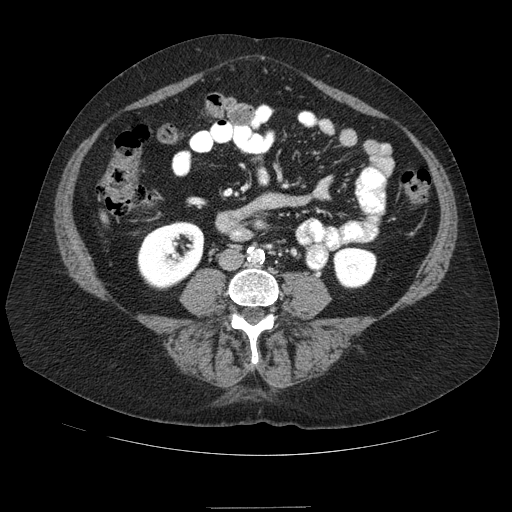
Contrast-enhanced abdominal CT (liver protocol), one axial slice; position 8 of 89 along the scan axis; reconstruction kernel STANDARD; 120 kVp; soft-tissue window (W 400 / L 40 HU); 2.5 mm slice thickness; 512 × 512 image matrix. Case-level facts recorded for this patient, not image findings: diagnosis: hepatocellular carcinoma (patient treated with transarterial chemoembolisation; whether this scan precedes or follows treatment is not stated here); TNM stage (as recorded): Stage-IIIB; Child-Pugh class: A; tumour nodularity: multinodular.
Outlined on this slice (semi-automatic segmentation, software-assisted and operator-edited):
- liver parenchyma outside the tumour (the mass and vessels are separate outlines, so this box may not span the whole liver): box from (x=100, y=212) to (x=107, y=222) px